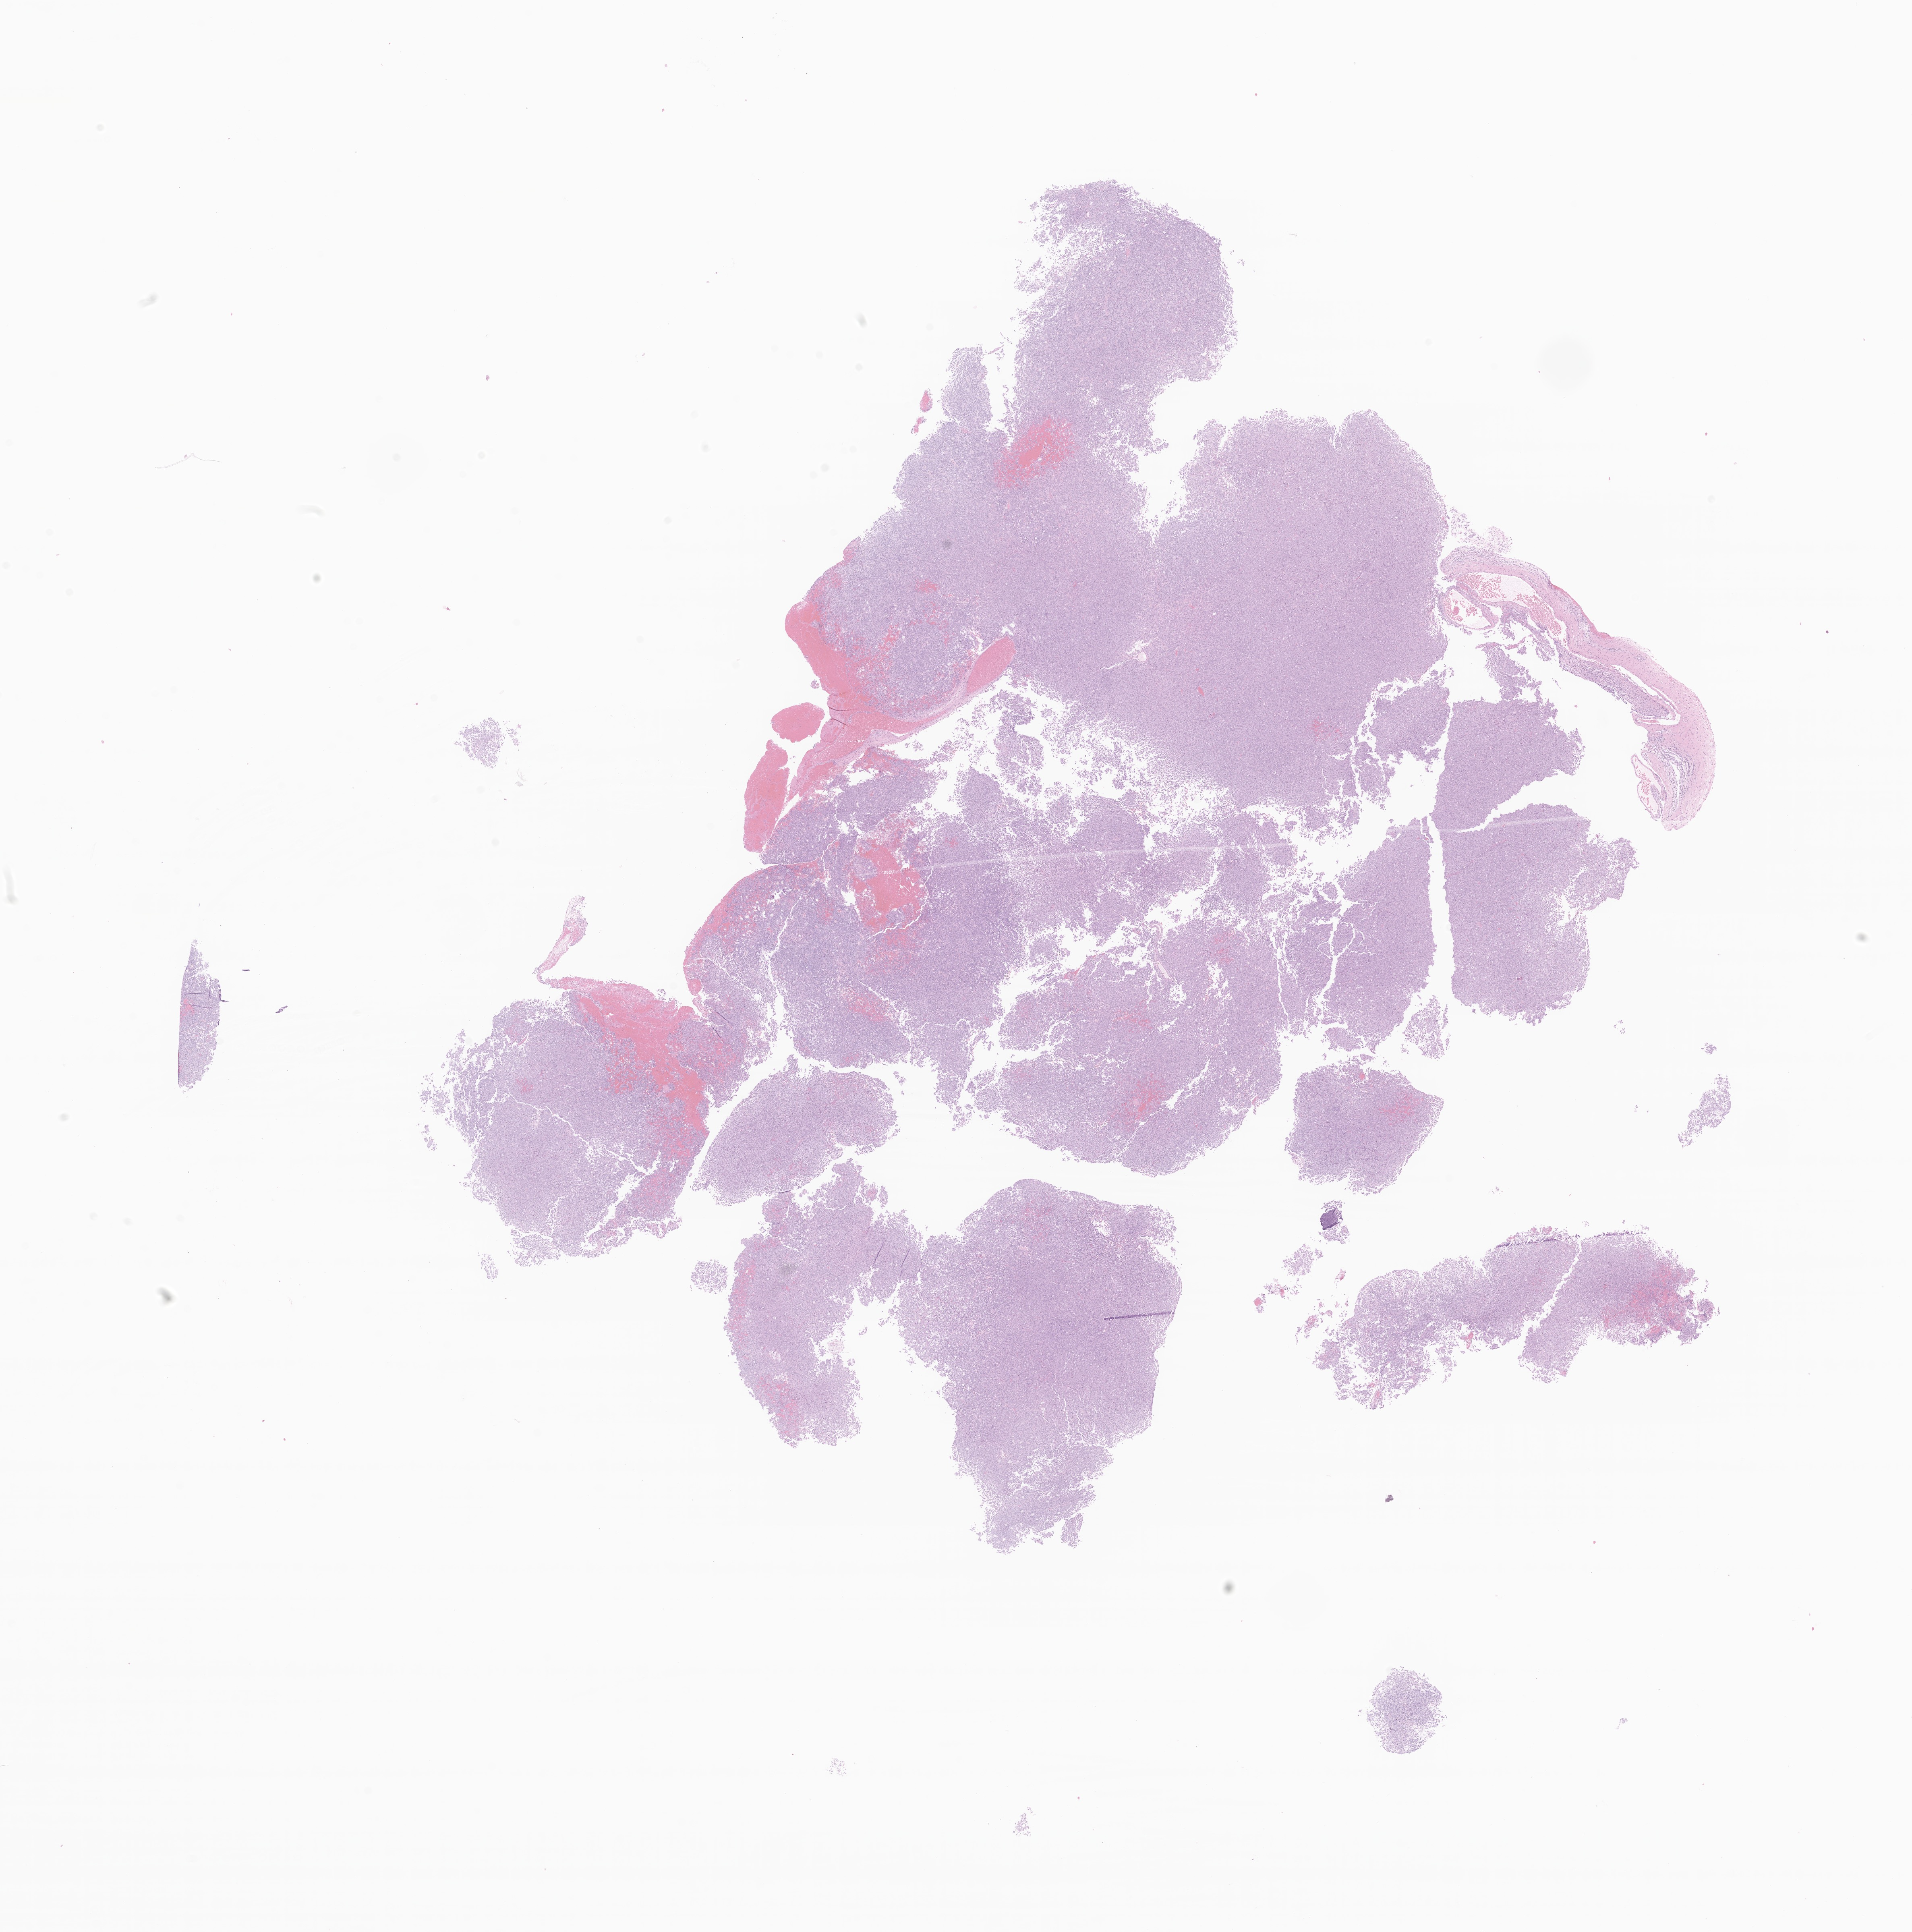
Whole-slide image, haematoxylin and eosin stain of tumor tissue from the cerebral ventricle — low-resolution overview of the scanned area, about 20.0 x 20.2 mm; FFPE section. Patient: male, age 40 months (3 years 4 months).
Diagnosis (ICD-O-3 morphology term): Astrocytoma, NOS.